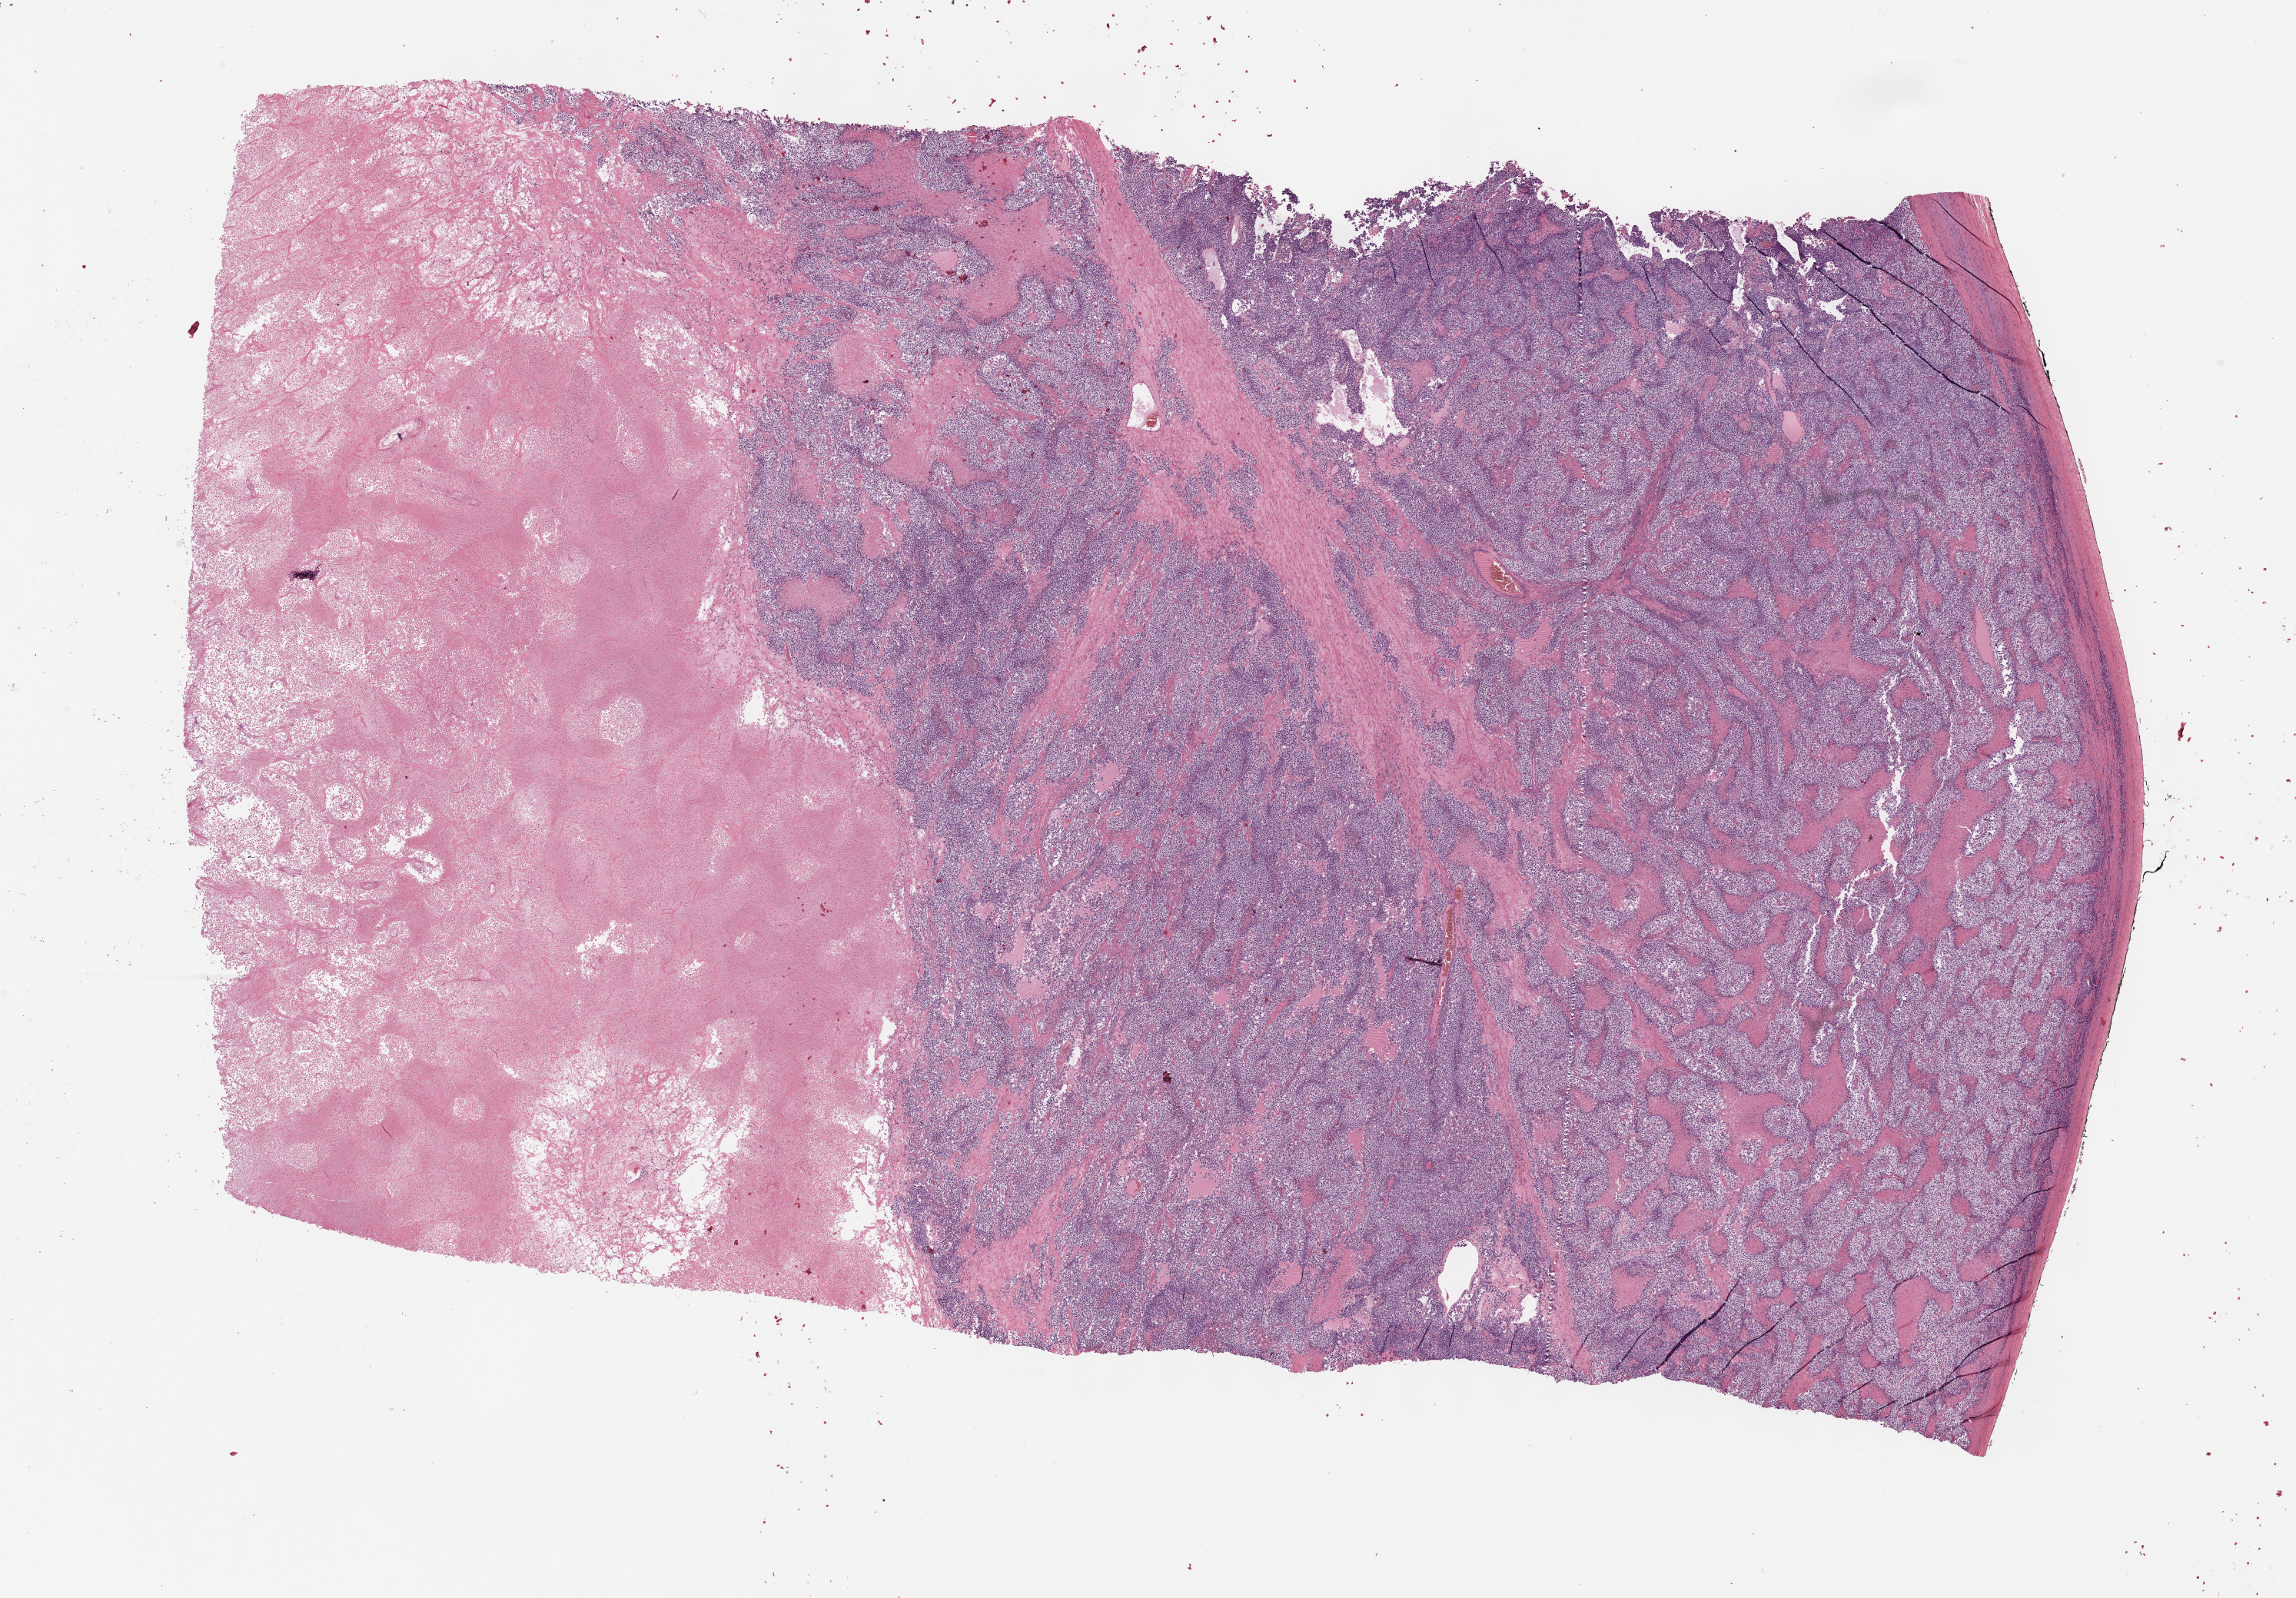
H&E whole-slide image, low-resolution overview of the scanned area, about 24.2 x 16.8 mm; formalin-fixed paraffin-embedded (FFPE) diagnostic section; sample: primary tumour, testis. Male patient; age at initial diagnosis 34 years.
Pathologic diagnosis: Seminoma, NOS.